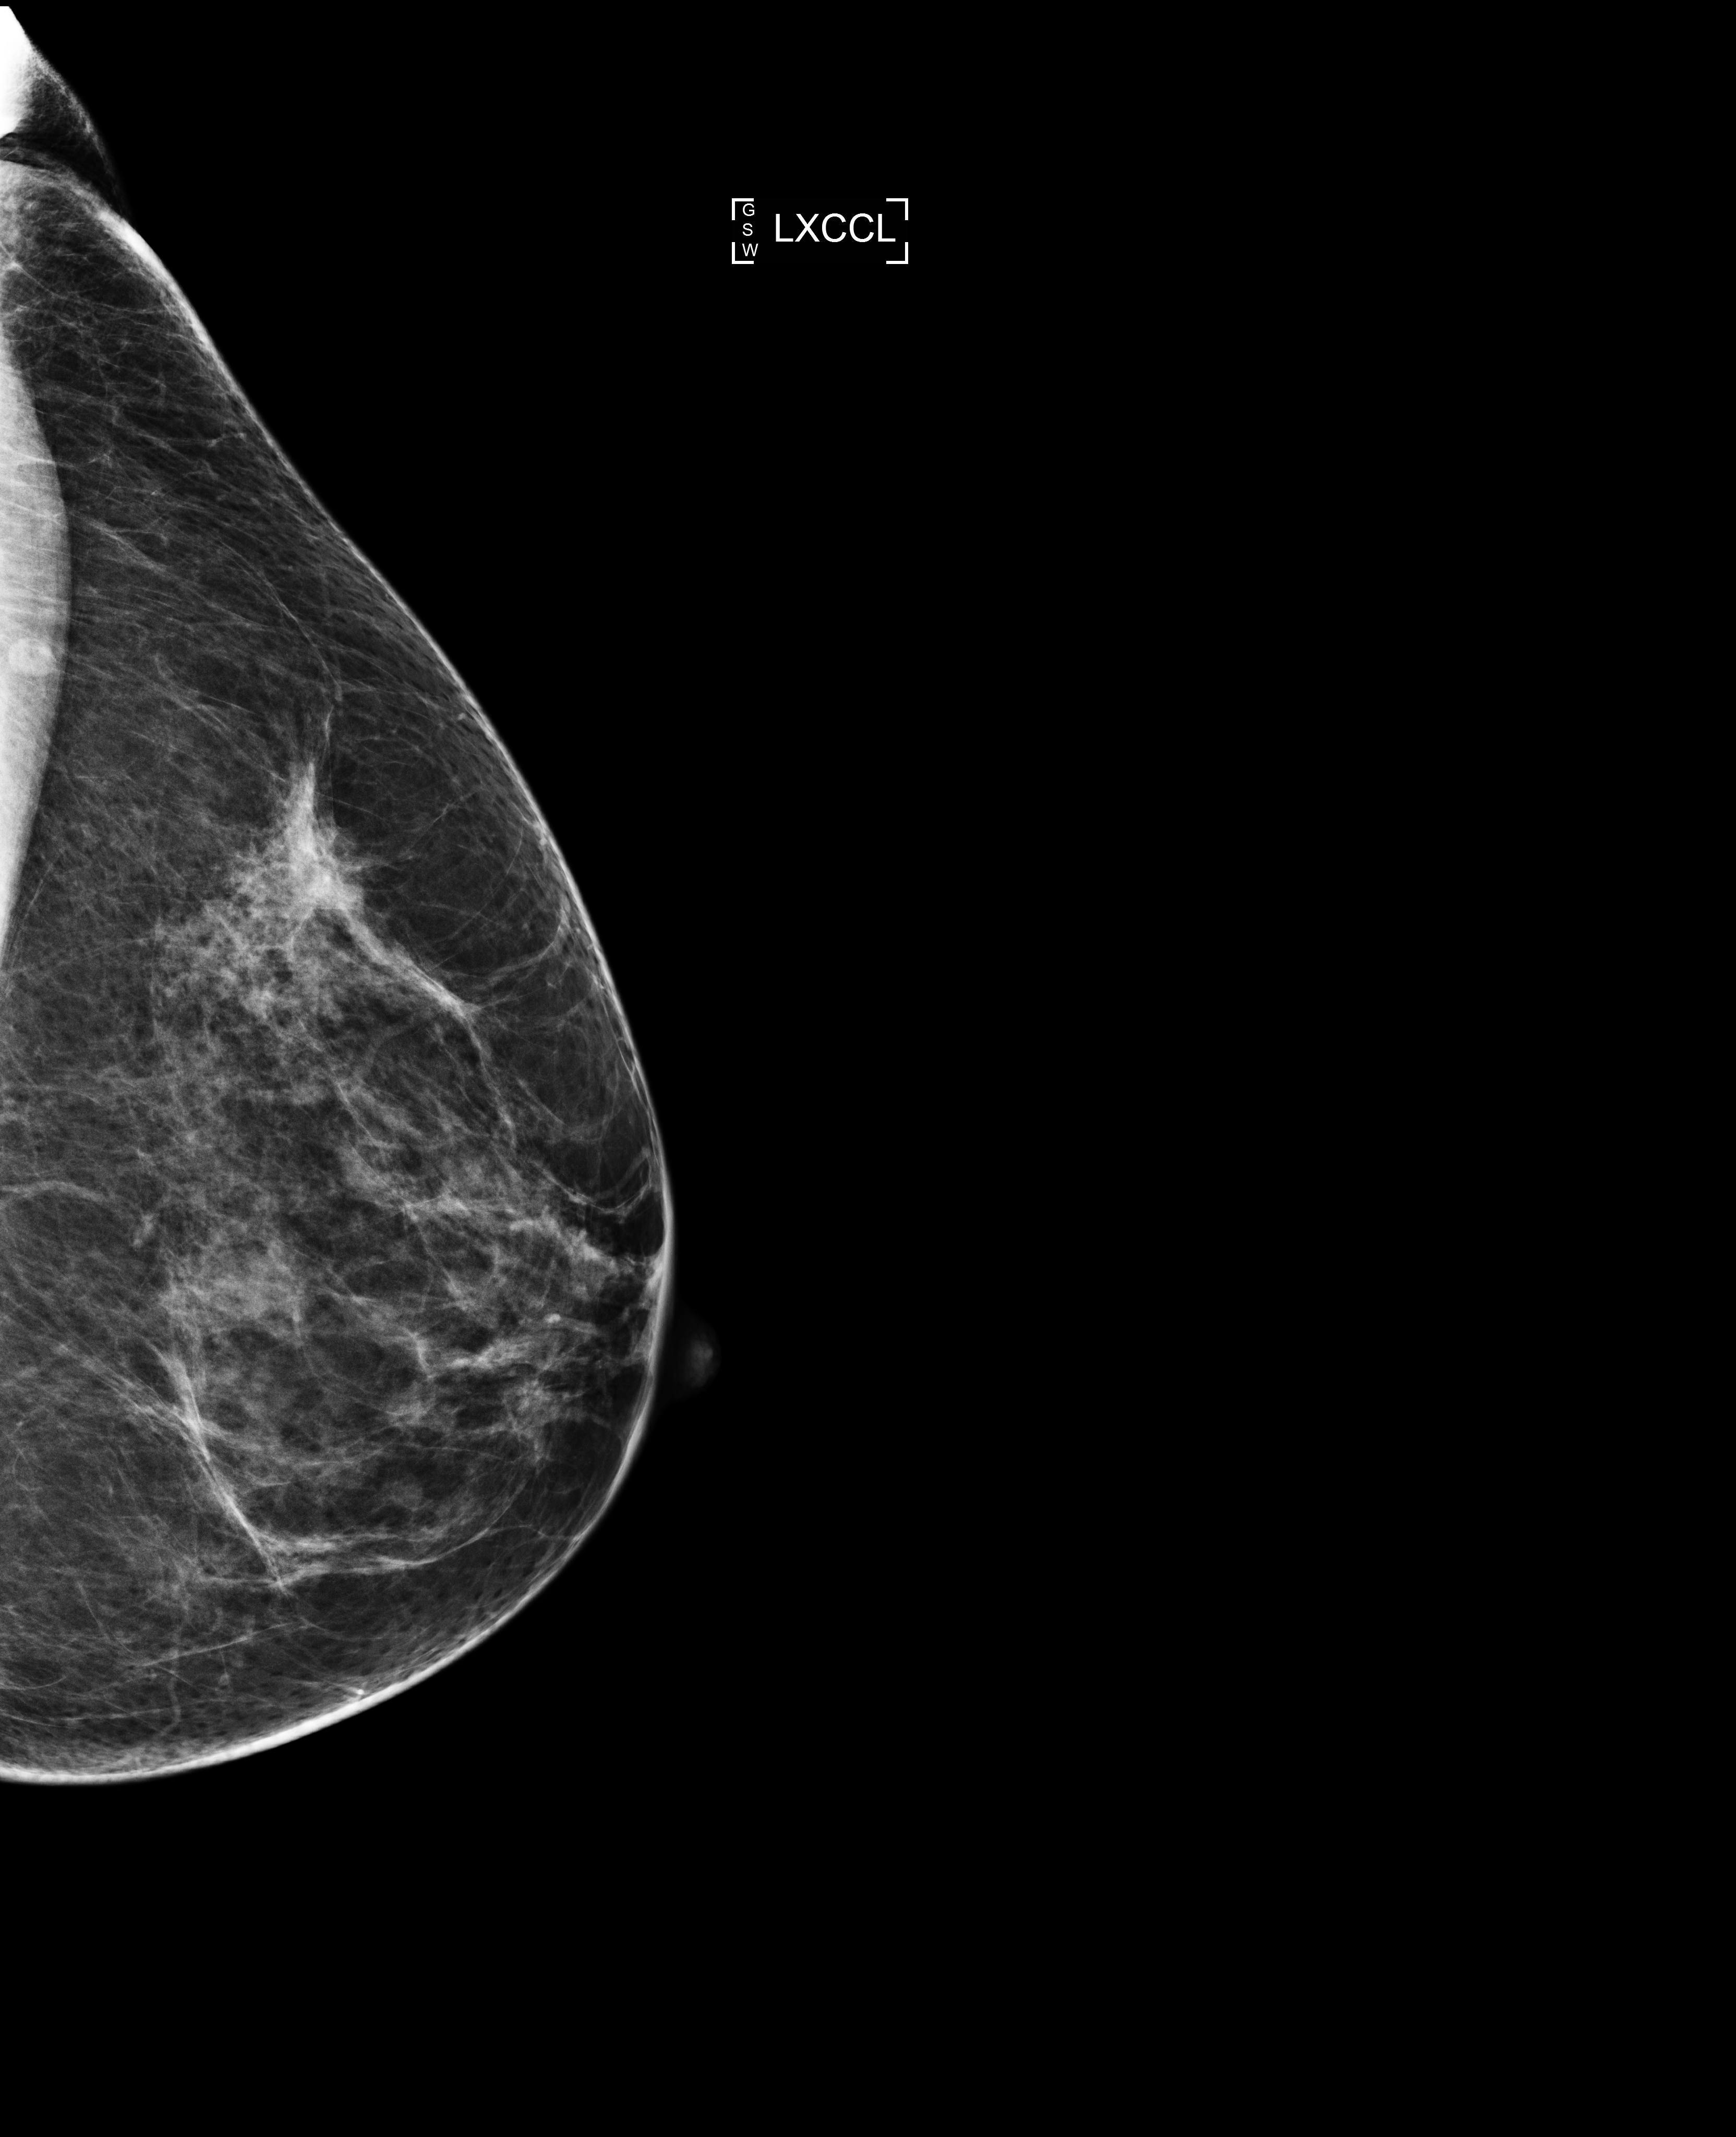
Screening examination, compressed breast thickness 70 mm, system: Selenia Dimensions. Female patient, age 51 years.
Image type: full-field digital mammogram. Breast: left. Projection: exaggerated CC view (lateral). BI-RADS breast density category at the screening exam (both breasts, scale 1–4): 3. Final BI-RADS category for the screening round (tomosynthesis exam, both breasts): category 1. Recall: no recall after this screen.